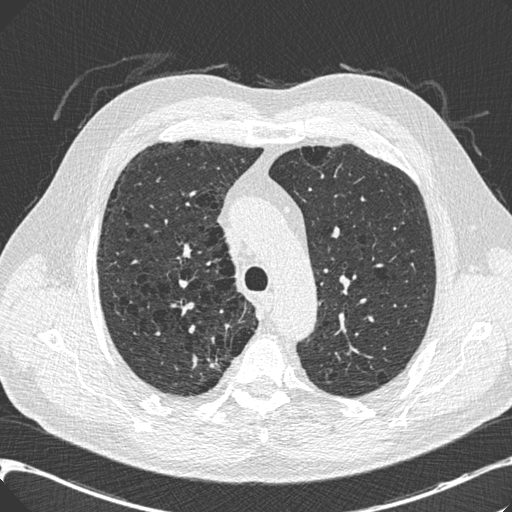
Axial slice from a low-dose chest CT screening exam. Third screening round (two years after baseline). Lung window (W 1500 / L -600 HU). 0.75 mm slice thickness. 120 kVp. Slice 53 of 197 in the series. 512 × 512 image matrix, field of view 367 × 367 mm. Male, age 68 years at enrolment. Current smoker at enrolment.
• Expert-annotated lung lesion, bounding box <189,344,237,381> (left, top, right, bottom; pixels).
• The screening reader recorded 3 non-calcified nodules or masses ≥4 mm on this exam (right upper lobe, right upper lobe, left lower lobe); which of them this box marks is not recorded.
• Lung cancer was diagnosed 46 days after this screen: adenocarcinoma, NOS, right upper lobe, well differentiated (G1), stage IB (AJCC 6th edition), 15 mm at pathology.